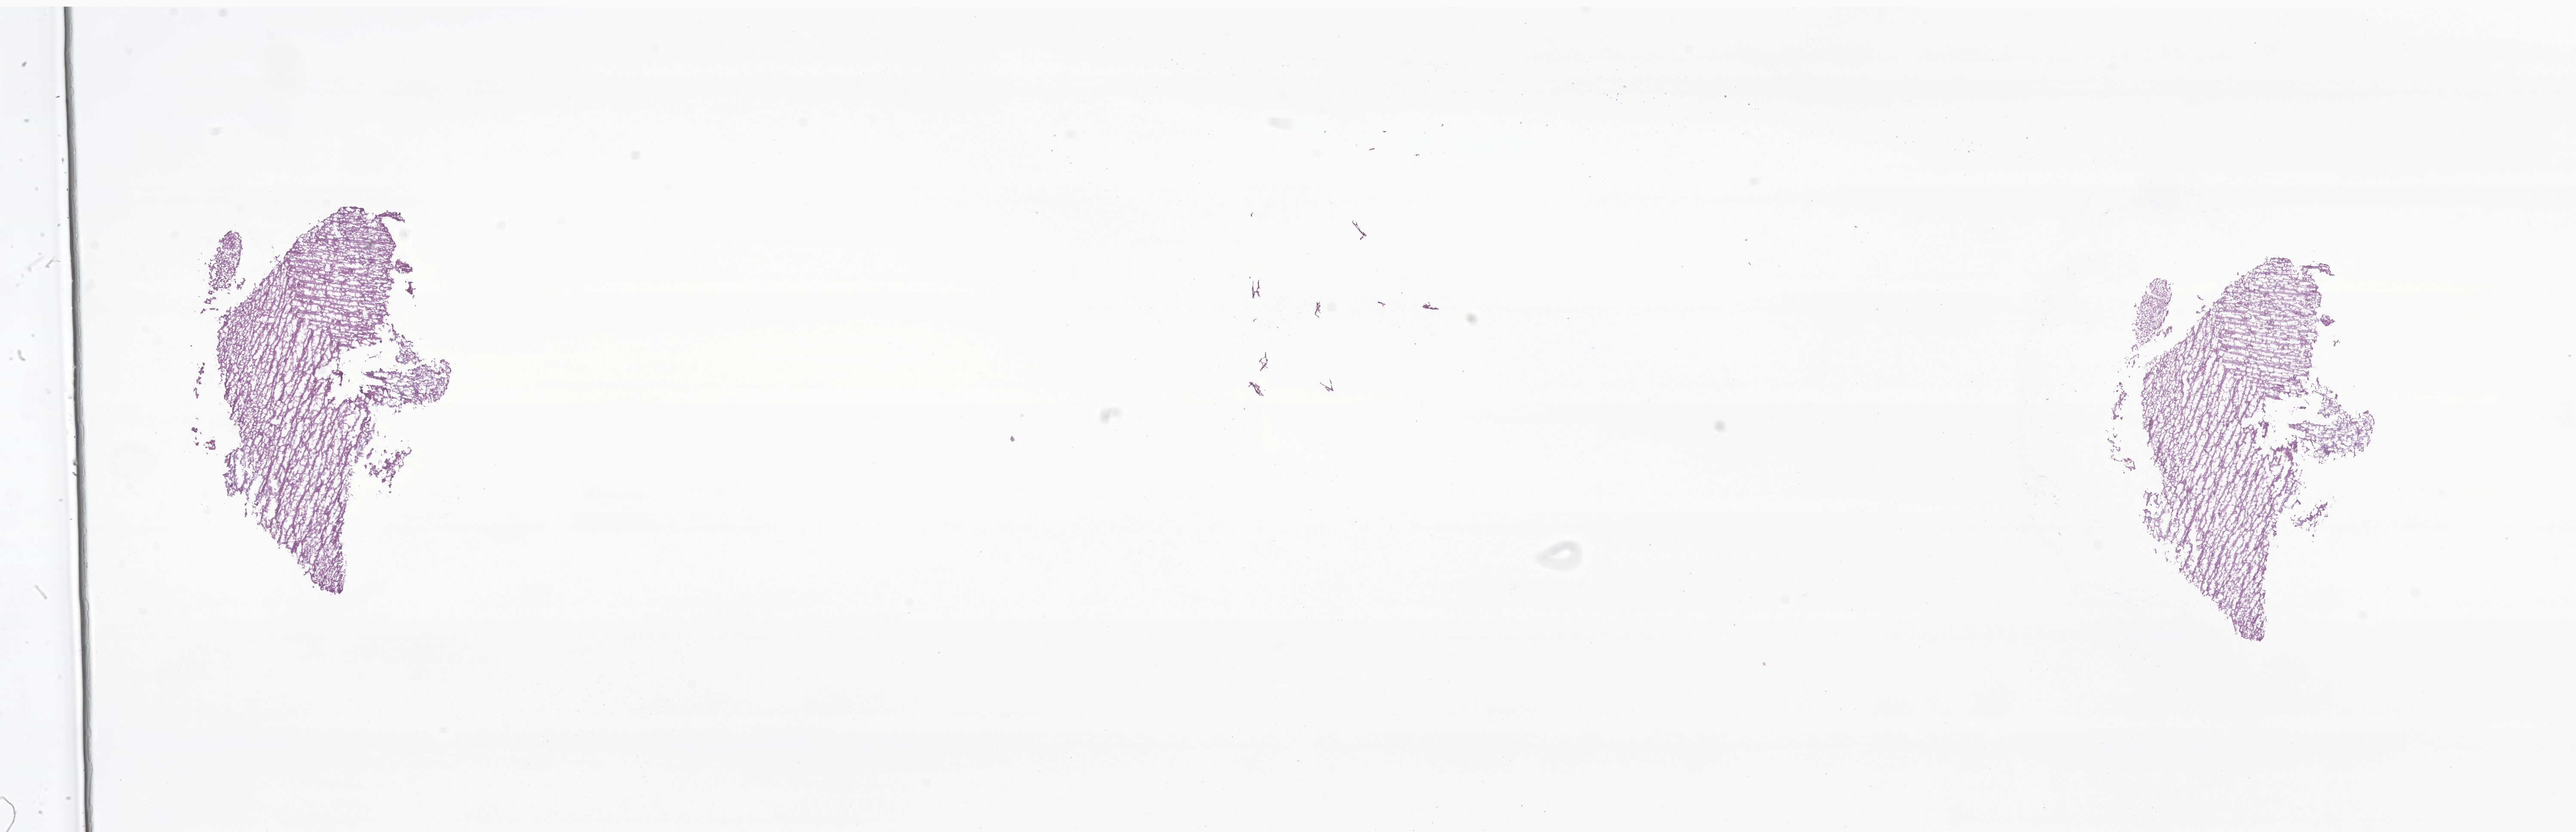
H&E whole-slide image of tumor tissue from the brain, shown as a low-resolution overview of the whole scanned area (about 25.3 x 8.2 mm), frozen section (OCT-embedded). Patient: male, age 78 months (6 years 6 months).
Diagnosis (ICD-O-3 morphology term): Dysembryoplastic neuroepithelial tumor.